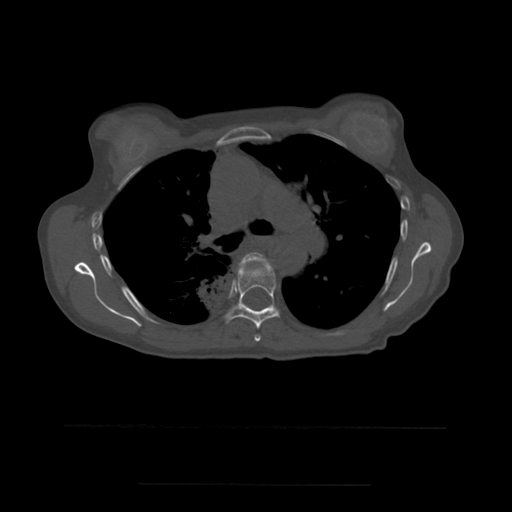
CT including the spine, one axial slice; slice 378 of 544 in the series (ordered by position); bone window (W 1800 / L 400 HU); 1.25 mm slice thickness; 512 × 512 image matrix, field of view 350 × 350 mm. Patient age 58 years. Case-level facts recorded for this patient, not image findings: primary cancer: lung.
Outlined on this slice (semi-automatically segmented with operator editing):
- T5 vertebra: bounding box <243,253,271,342> (left, top, right, bottom; pixels)
- T6 vertebra: <221,258,280,329>